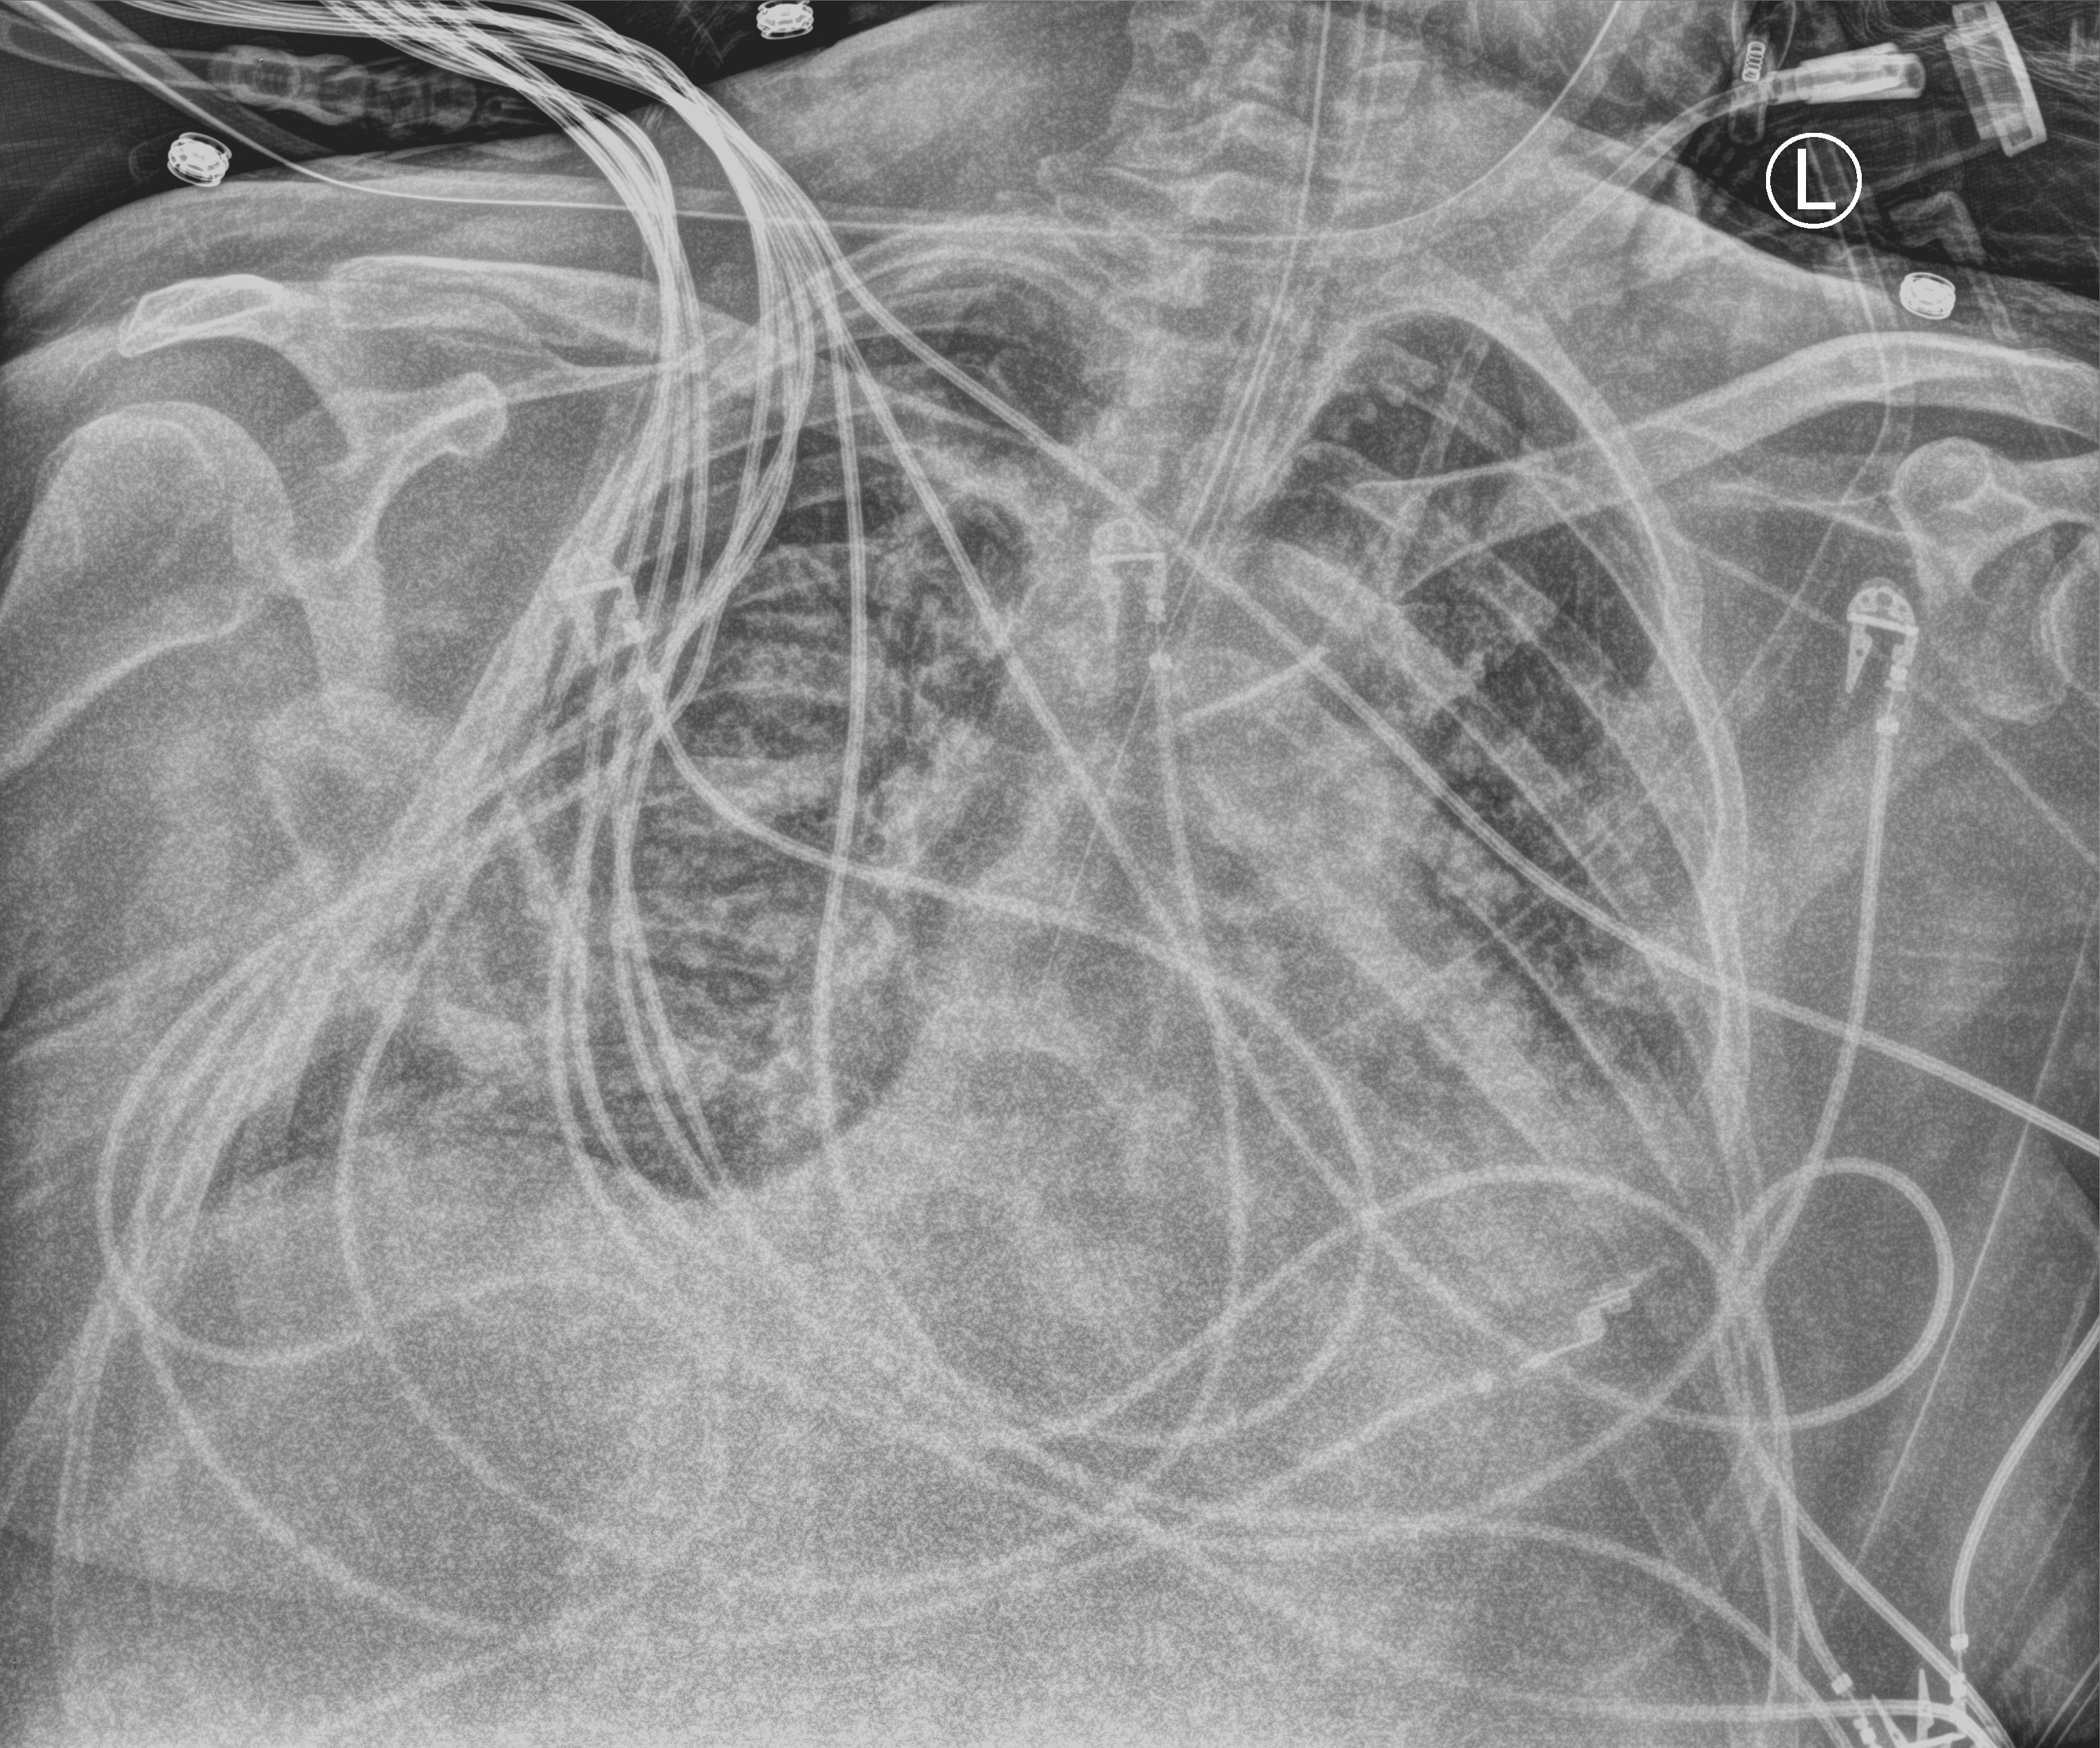
Bedside chest radiograph (computed radiography); anteroposterior (AP) projection. Patient hospitalised with COVID-19; male, aged 18–59 years.
Hospital-stay facts (about this admission, not read from this image; timing relative to this image not recorded):
- diabetes (admission record): no